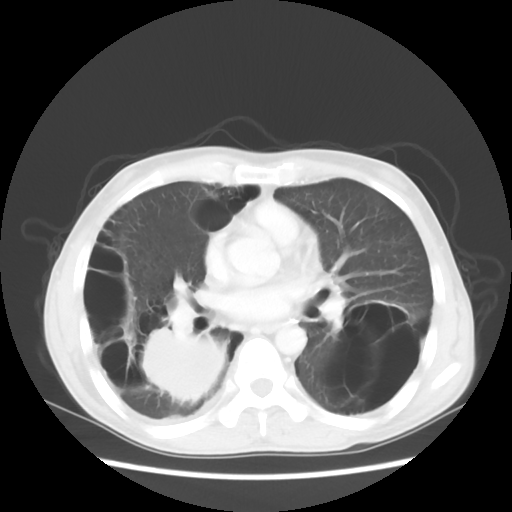
Chest CT, one axial slice; slice 27 of 56 in the series (ordered by position); reconstruction kernel STANDARD; lung window (W 1500 / L -600 HU); 5 mm slice thickness; 512 × 512 image matrix, field of view 351 × 351 mm. Patient: male, 41 years. Case-level facts recorded for this patient, not image findings: clinical TNM (as recorded): T4 N0 M1a; histopathological grade: G3.
Structures marked on this image (bounding box drawn by a radiologist):
- lung tumour (recorded histology: large cell carcinoma): bounding box (x1, y1, x2, y2) in pixels: (138, 322, 235, 407)